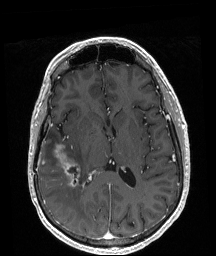
Brain MRI from a brain-tumour surgery series, one axial slice. Slice 98 of 208 in the series (ordered by position). T1-weighted post-contrast. 216 × 256 image matrix, field of view 211 × 250 mm. Case-level facts recorded for this patient, not image findings: histopathology: Astrocytoma; WHO grade: 4; IDH mutation: yes; tumour location: Right Temporal.
Structures marked on this image (manually delineated by an expert):
- tumour: bounding box (x1, y1, x2, y2) in pixels: (53, 144, 80, 187)